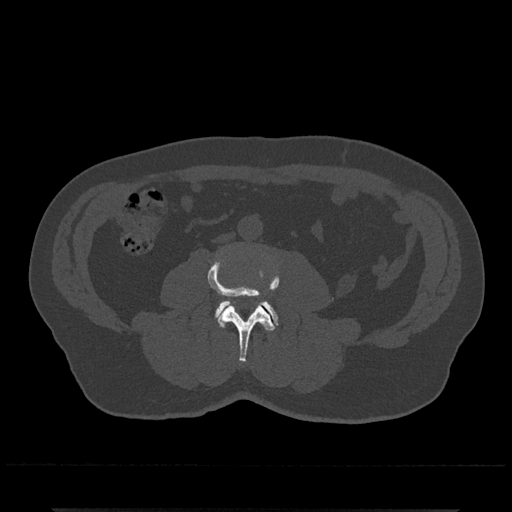
CT including the spine, one axial slice. Slice 203 of 797 in the series (ordered by position). Reconstruction kernel Br40s/3. Bone window (W 1800 / L 400 HU). 0.5 mm slice thickness. 512 × 512 image matrix, field of view 393 × 393 mm. Patient: male, 67 years. From the clinical record (not read from this slice): primary cancer: prostate.
Annotated regions visible in this slice (semi-automatic segmentation, software-assisted and operator-edited):
- L3 vertebra: bounding box [x1, y1, x2, y2] px = [208, 257, 280, 362]
- L4 vertebra: [215, 300, 279, 326]